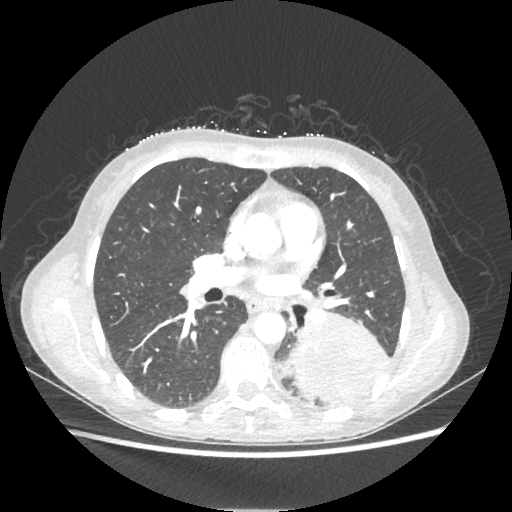
Chest CT, one axial slice; slice 118 of 221 in the series (ordered by position); lung window (W 1500 / L -600 HU); 512 × 512 image matrix, field of view 360 × 360 mm. Patient: female, 53 years. Case-level facts recorded for this patient, not image findings: clinical TNM (as recorded): T3 N0 M0.
Outlined on this slice (bounding box drawn by a radiologist):
- lung tumour (recorded histology: adenocarcinoma): box from (x=287, y=308) to (x=388, y=403) px